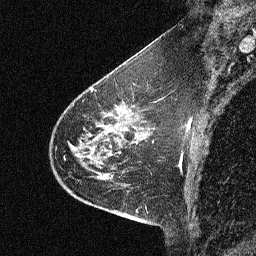
Breast MRI (dynamic contrast-enhanced), one sagittal slice. Position 19 of 64 along the scan axis. Dynamic contrast-enhanced study with each time point stored as its own series, time point 2 of 3 at this slice position (early post-contrast, ordered by acquisition time). 1.5 T. TE 4.5 ms, TR 11 ms. 256 × 256 image matrix, field of view 200 × 200 mm. Female patient, age 46 years. From the clinical record (not read from this slice): setting: breast cancer imaged before/during neoadjuvant chemotherapy; receptor status: HER2-positive.
Outlined on this slice (semi-automatically segmented with operator editing):
- analysis volume of interest (the breast-tissue region the enhancement analysis was run in; not a lesion): box from (x=42, y=80) to (x=150, y=180) px
- tumour enhancement mask (voxels above the 90 % enhancement threshold inside the analysis volume of interest): (x=68, y=104)–(x=135, y=159)